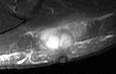
MRI of an extremity soft-tissue mass, one axial slice; slice 14 of 36 in the series (ordered by position); STIR; MR volume resampled by the dataset authors to the PET/CT grid (not the native acquisition matrix); 3.27 mm slice thickness; 116 × 74 image matrix. Male patient. Case-level facts recorded for this patient, not image findings: histological type: pleiomorphic leiomyosarcoma; grade: high; site of the primary tumour: left buttock.
Structures marked on this image (expert contour drawn on MRI and transferred to this co-registered scan by the dataset authors):
- gross tumour volume including surrounding oedema: bounding box [x1, y1, x2, y2] px = [30, 19, 83, 52]
- gross tumour volume (mass): [34, 21, 81, 52]